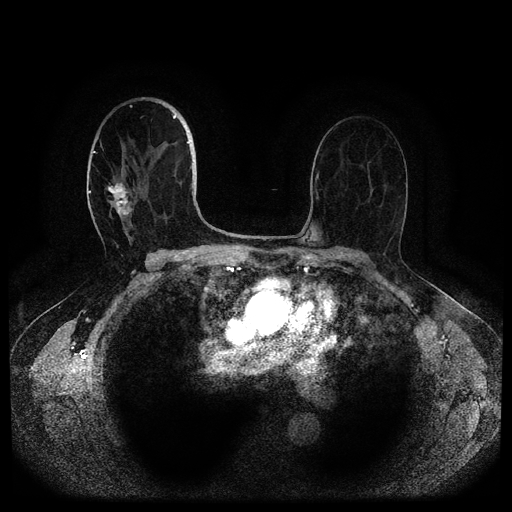
Breast MRI (dynamic contrast-enhanced, multi-phase), one axial slice. Position 61 of 116 along the scan axis. Dynamic contrast-enhanced series, time point 2 of 5 at this slice position (early post-contrast). 1.5 T. TE 2.6 ms, TR 5.3 ms. 512 × 512 image matrix, field of view 350 × 350 mm. Patient: female, 82 years.
Structures marked on this image (semi-automatically segmented with operator editing):
- breast lesion (labelled 'tumour' in the annotation; benign lesions carry a separate 'benign' label): bounding box [x1, y1, x2, y2] px = [106, 178, 135, 219]